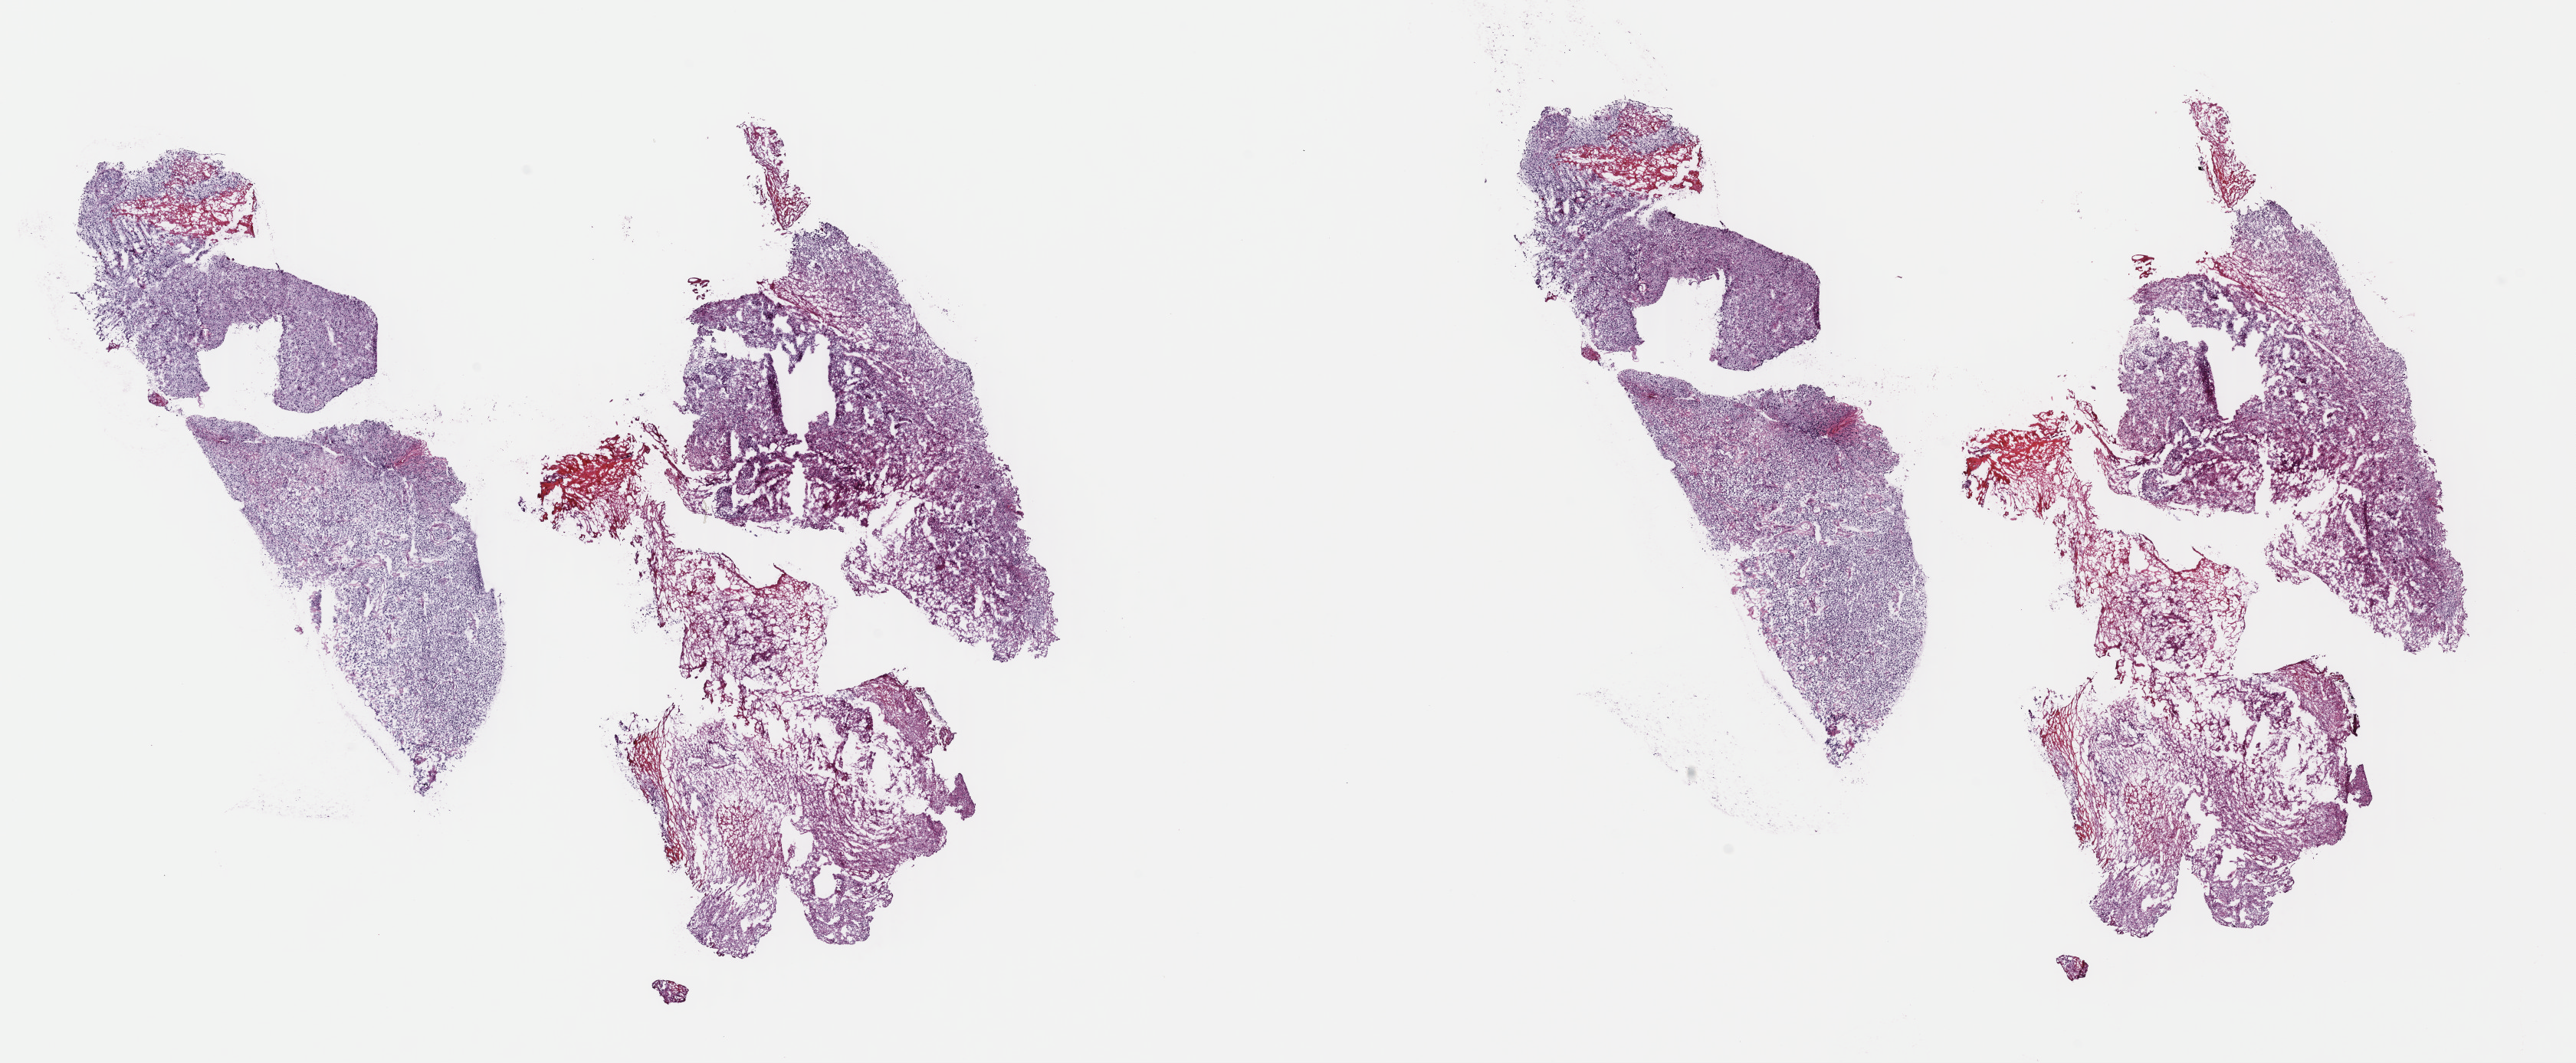
Whole-slide histology image, H&E — low-resolution overview of the scanned area, about 26.4 x 10.9 mm. Frozen section from the top of the tissue portion. Brain, primary tumour sample. Female patient; age at initial diagnosis 58 years. Histologic grade: G3 (poorly differentiated). Slide review estimates, as recorded: tumour cells 50%, tumour nuclei 80%, normal cells 5%, stromal cells 30%, necrosis 15%. Infiltration values recorded for this section: lymphocyte infiltration 0%, monocyte infiltration 0%, neutrophil infiltration 0%.
* pathologic diagnosis: Oligodendroglioma, anaplastic (cerebrum)
* laterality: right